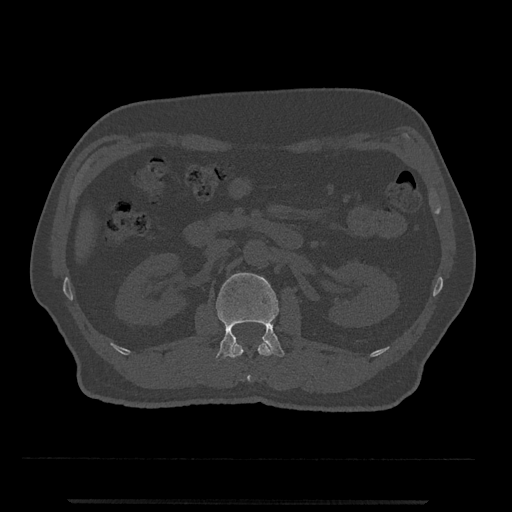
CT including the spine, one axial slice. Position 290 of 797 along the scan axis. Reconstruction kernel Br40s/3. Bone window (W 1800 / L 400 HU). 0.5 mm slice thickness. 512 × 512 image matrix, field of view 419 × 419 mm. Male patient, age 63 years. From the clinical record (not read from this slice): primary cancer: prostate.
Annotated regions visible in this slice (semi-automatic segmentation, software-assisted and operator-edited):
- L1 vertebra: bounding box <229,342,273,382> (left, top, right, bottom; pixels)
- L2 vertebra: <216,272,285,361>